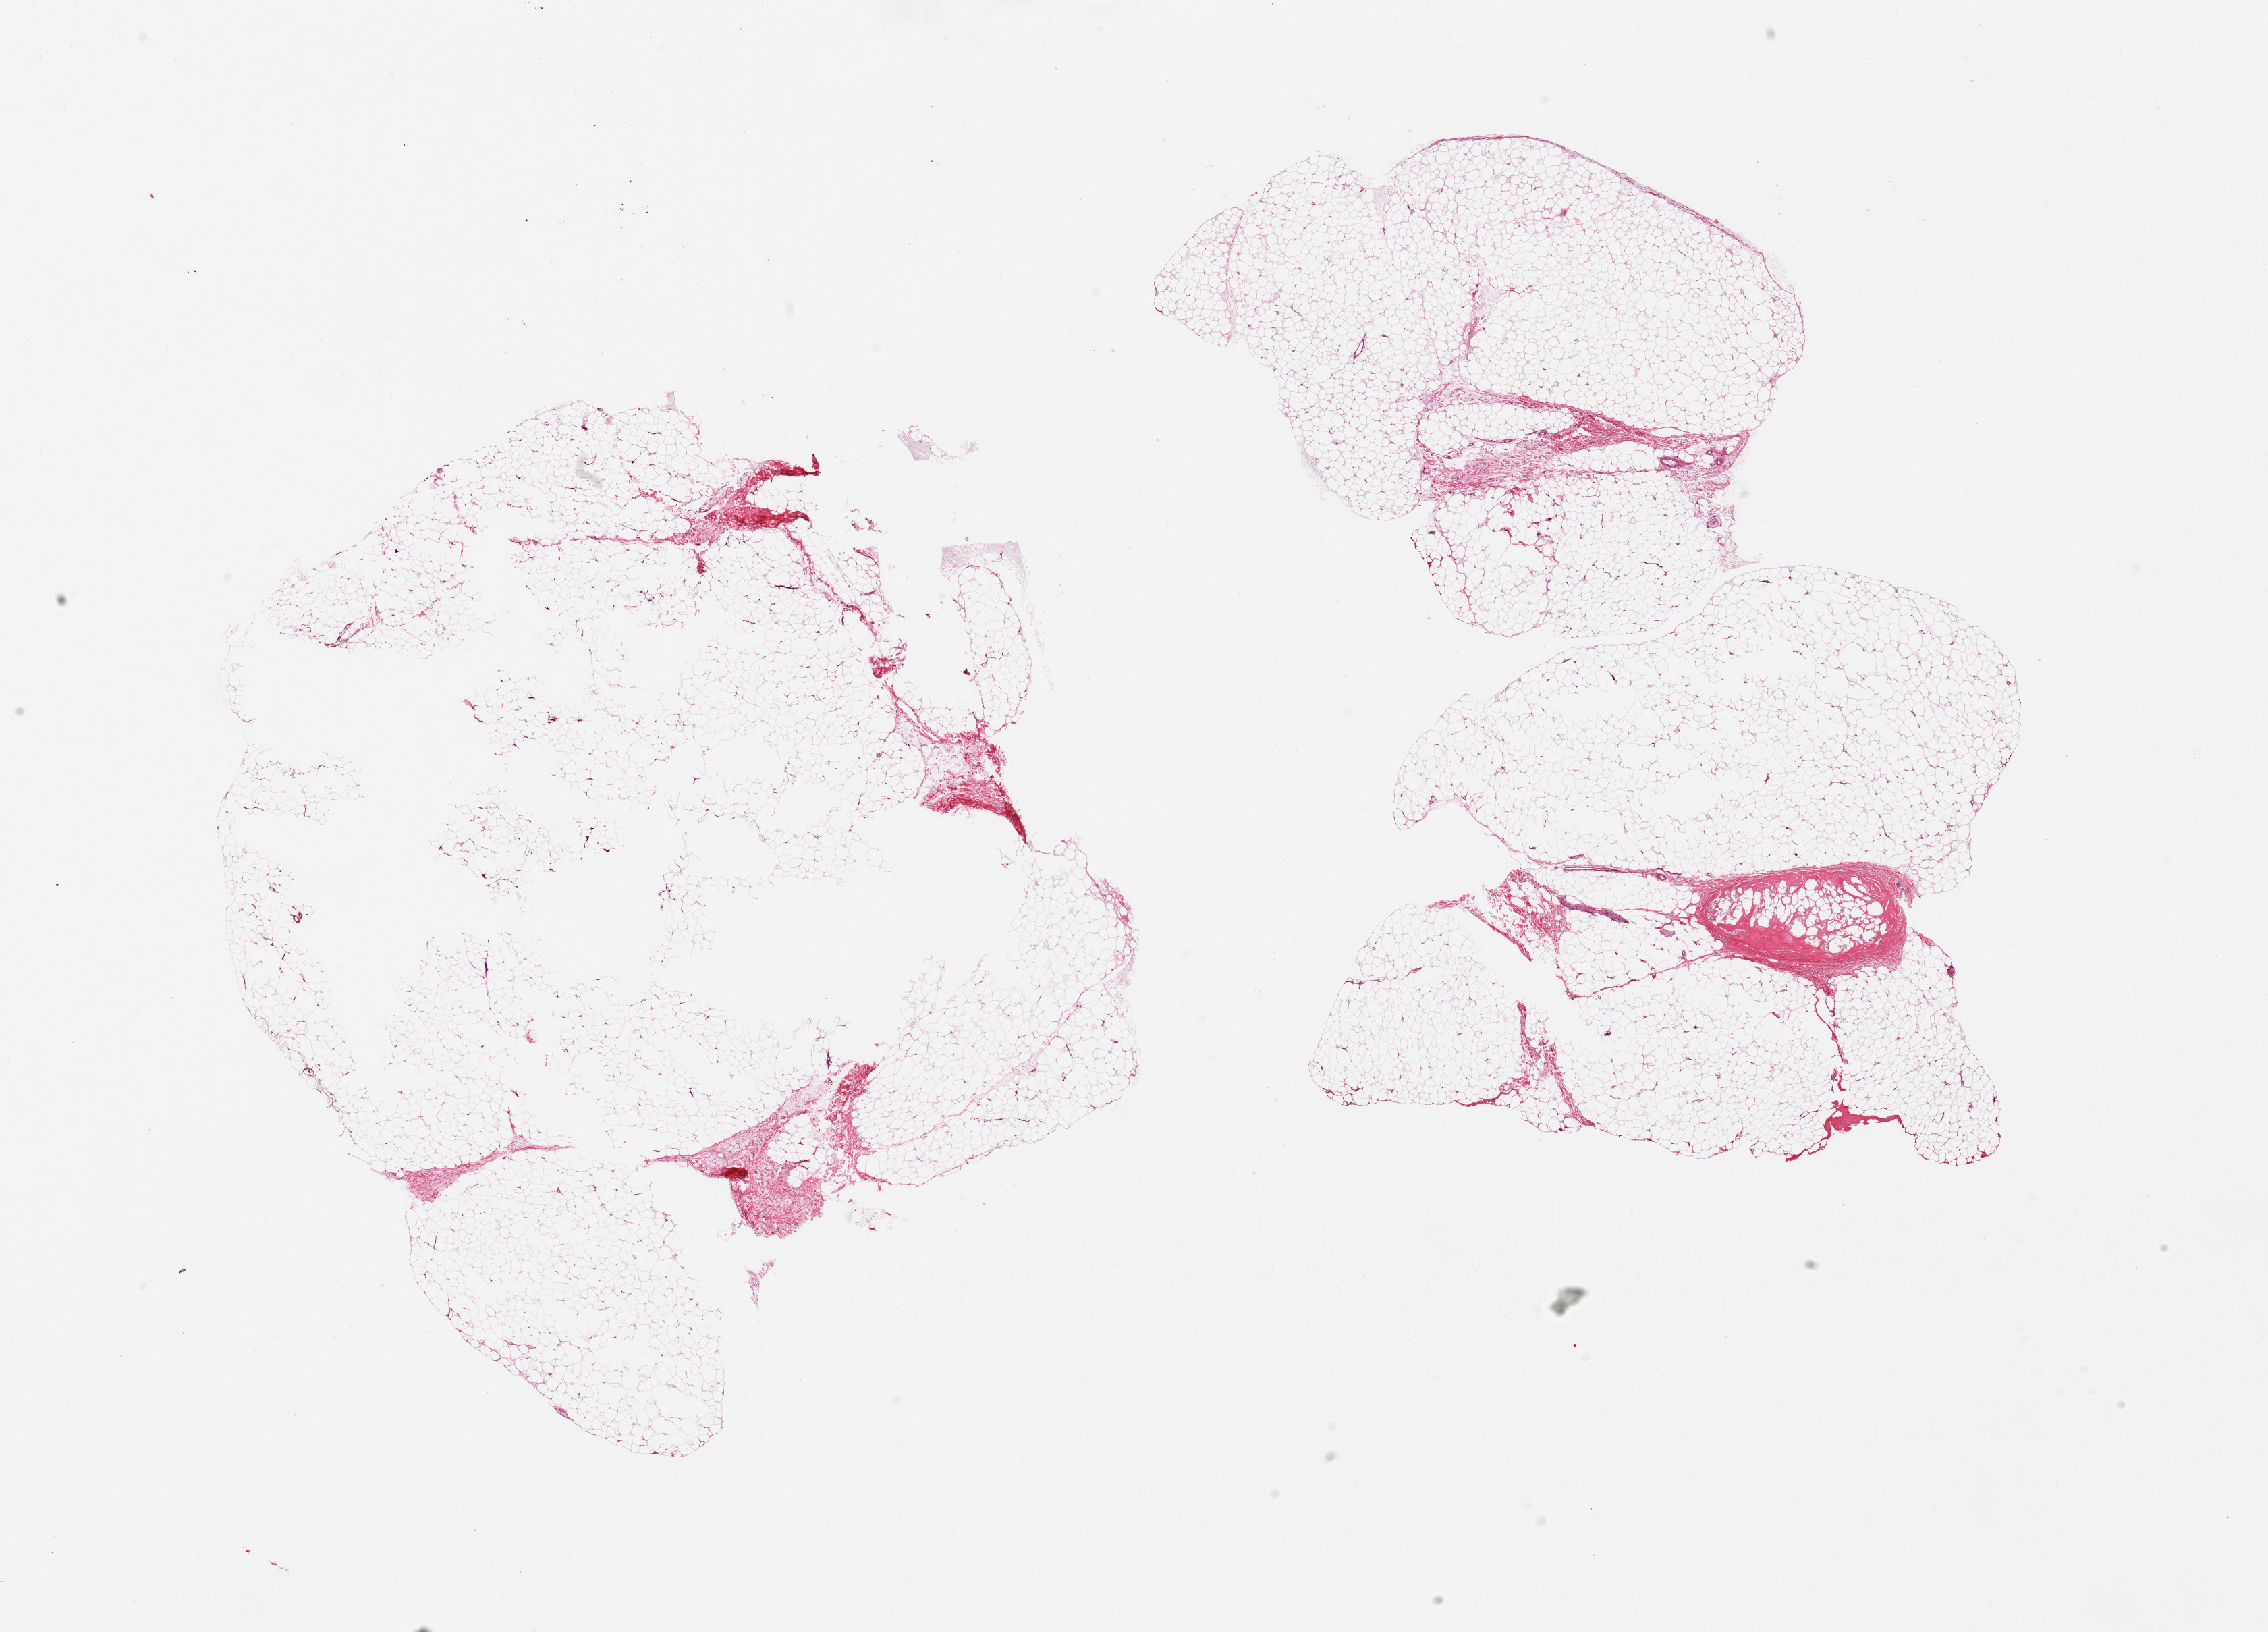
Whole-slide image, haematoxylin and eosin stain, whole scanned area (about 26.6 x 19.1 mm, acquisition: 20x scan) shown as a low-resolution overview; PAXgene-fixed paraffin-embedded (PFPE) section; sampled site (target tissue): adipose tissue; tissue donor sample. Donor sex: female.
Review note (as recorded): 2 pieces; 5% fibrous content.